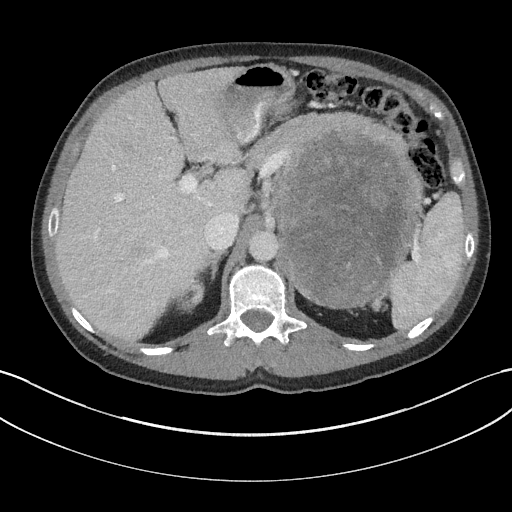
Contrast-enhanced abdominal CT, one axial slice. Slice 118 of 147 in the series (ordered by position). Reconstruction kernel I31f/3. Soft-tissue window (W 400 / L 40 HU). 3 mm slice thickness. 512 × 512 image matrix. Patient: male, 58 years. Case-level facts recorded for this patient, not image findings: diagnosis: adrenocortical carcinoma; tumour side: left adrenal.
Annotated regions visible in this slice (semi-automatically segmented with operator editing):
- mass: bounding box (x1, y1, x2, y2) in pixels: (278, 135, 414, 307)